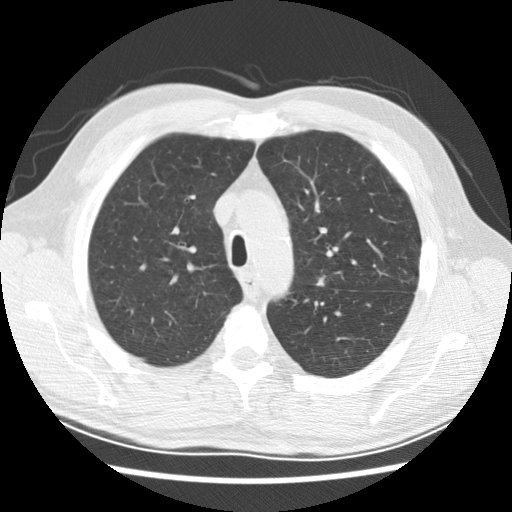
Low-dose screening chest CT, axial slice, baseline screening round, lung window (W 1500 / L -600 HU), slice 59 of 236 in the series. Male participant, aged 59 years at enrolment. Current smoker at enrolment.
• Expert reader's lesion annotation, bounding box [x1, y1, x2, y2] px = [302, 267, 341, 296].
• The exam's reader record, not a measurement of the box and not confirmed to be the same lesion: non-calcified nodule or mass ≥4 mm, left upper lobe, 8 × 5 mm, smooth margins, soft tissue attenuation.
• Lung cancer was diagnosed 645 days after this screen (after the second annual screen): adenocarcinoma, NOS, left upper lobe, left lower lobe, poorly differentiated (G3), stage IV (AJCC 6th edition).